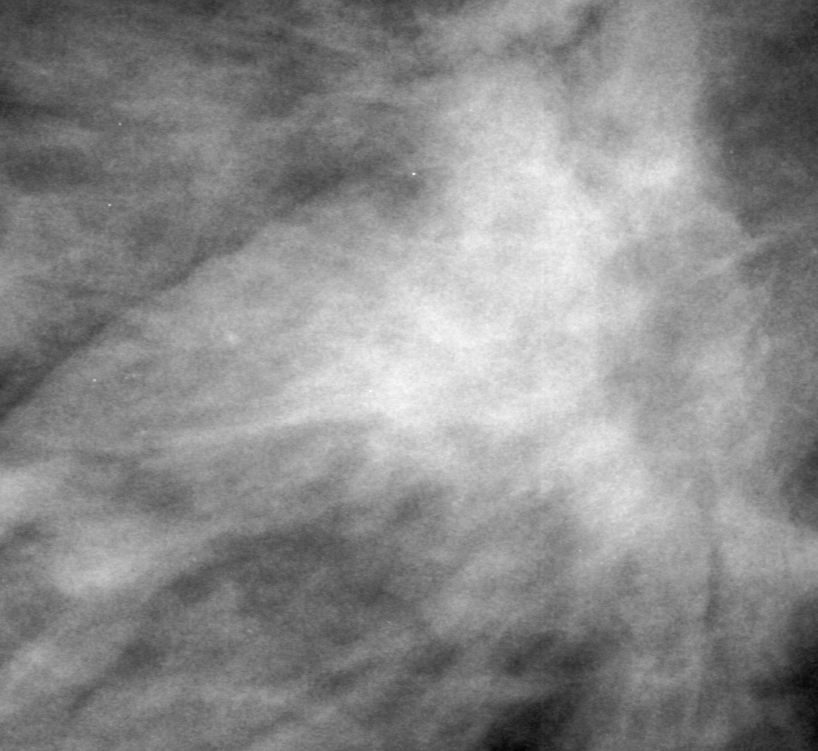
Region of interest cut from a scanned film mammogram (one marked finding), left breast, MLO view, BI-RADS breast density category 4 (scale 1–4).
Finding: mass, shape architectural distortion, margins spiculated; BI-RADS assessment category 2; benign; no additional work-up was recommended (benign without callback).